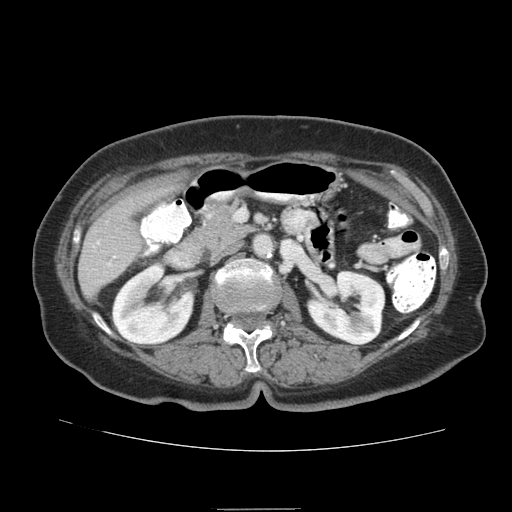
Contrast-enhanced abdominal CT (liver protocol), one axial slice; slice 31 of 95 in the series (ordered by position); reconstruction kernel STANDARD; 140 kVp; soft-tissue window (W 400 / L 40 HU); 2.5 mm slice thickness; 512 × 512 image matrix, field of view 360 × 360 mm. Case-level facts recorded for this patient, not image findings: diagnosis: hepatocellular carcinoma (patient treated with transarterial chemoembolisation; whether this scan precedes or follows treatment is not stated here); TNM stage (as recorded): Stage-IVA; Child-Pugh class: B; tumour differentiation: moderately differentiated.
Outlined on this slice (semi-automatically segmented with operator editing):
- liver parenchyma outside the tumour (the mass and vessels are separate outlines, so this box may not span the whole liver): bounding box <78,178,180,298> (left, top, right, bottom; pixels)
- liver vessels: <108,263,110,265>